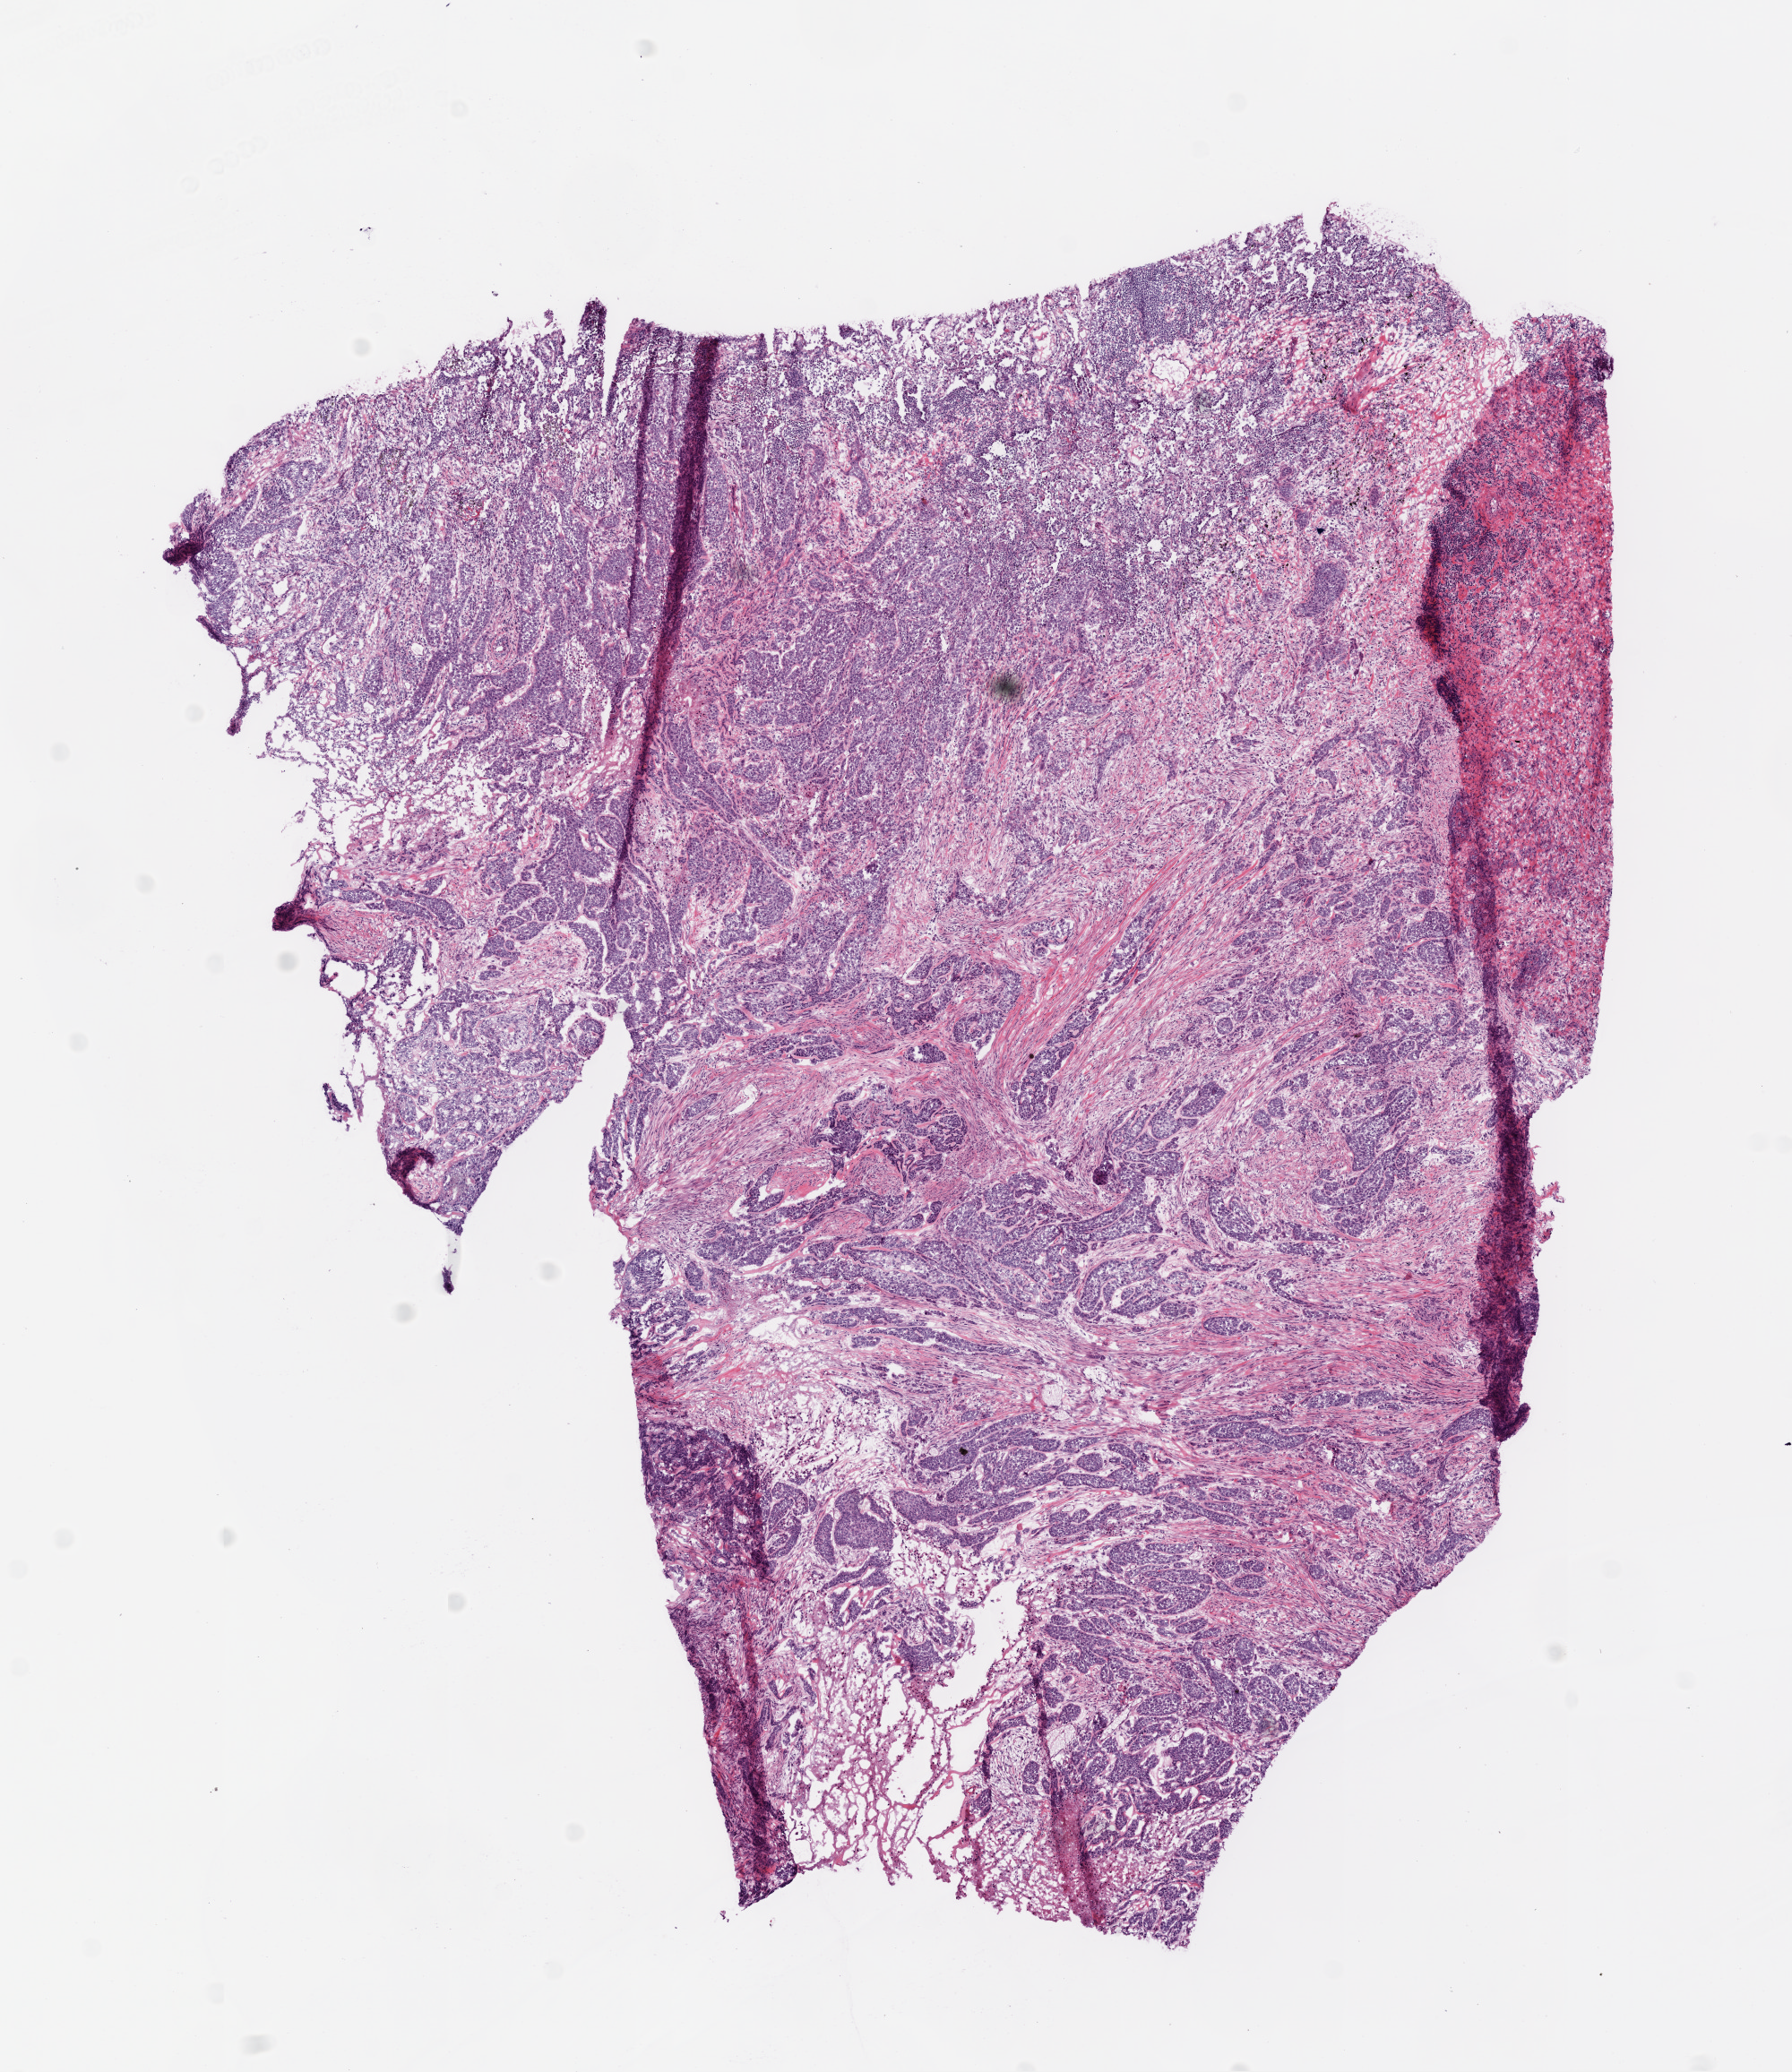
Whole-slide histology image, Hematoxylin and eosin (H&E) stained, whole scanned area (about 8.0 x 9.3 mm, slide scanned at 20x) shown as a low-resolution overview. Frozen section. Sample: primary tumour, lung. Male, age 75 years at initial diagnosis. Slide review estimates, as recorded: tumour cells 72%, tumour nuclei 70%, normal cells 0%, stromal cells 20%, necrosis 8%.
• TNM: T4 N0 M0
• pathologic diagnosis: Squamous cell carcinoma, NOS (upper lobe, lung)
• AJCC pathologic stage: IIIB (6th edition)